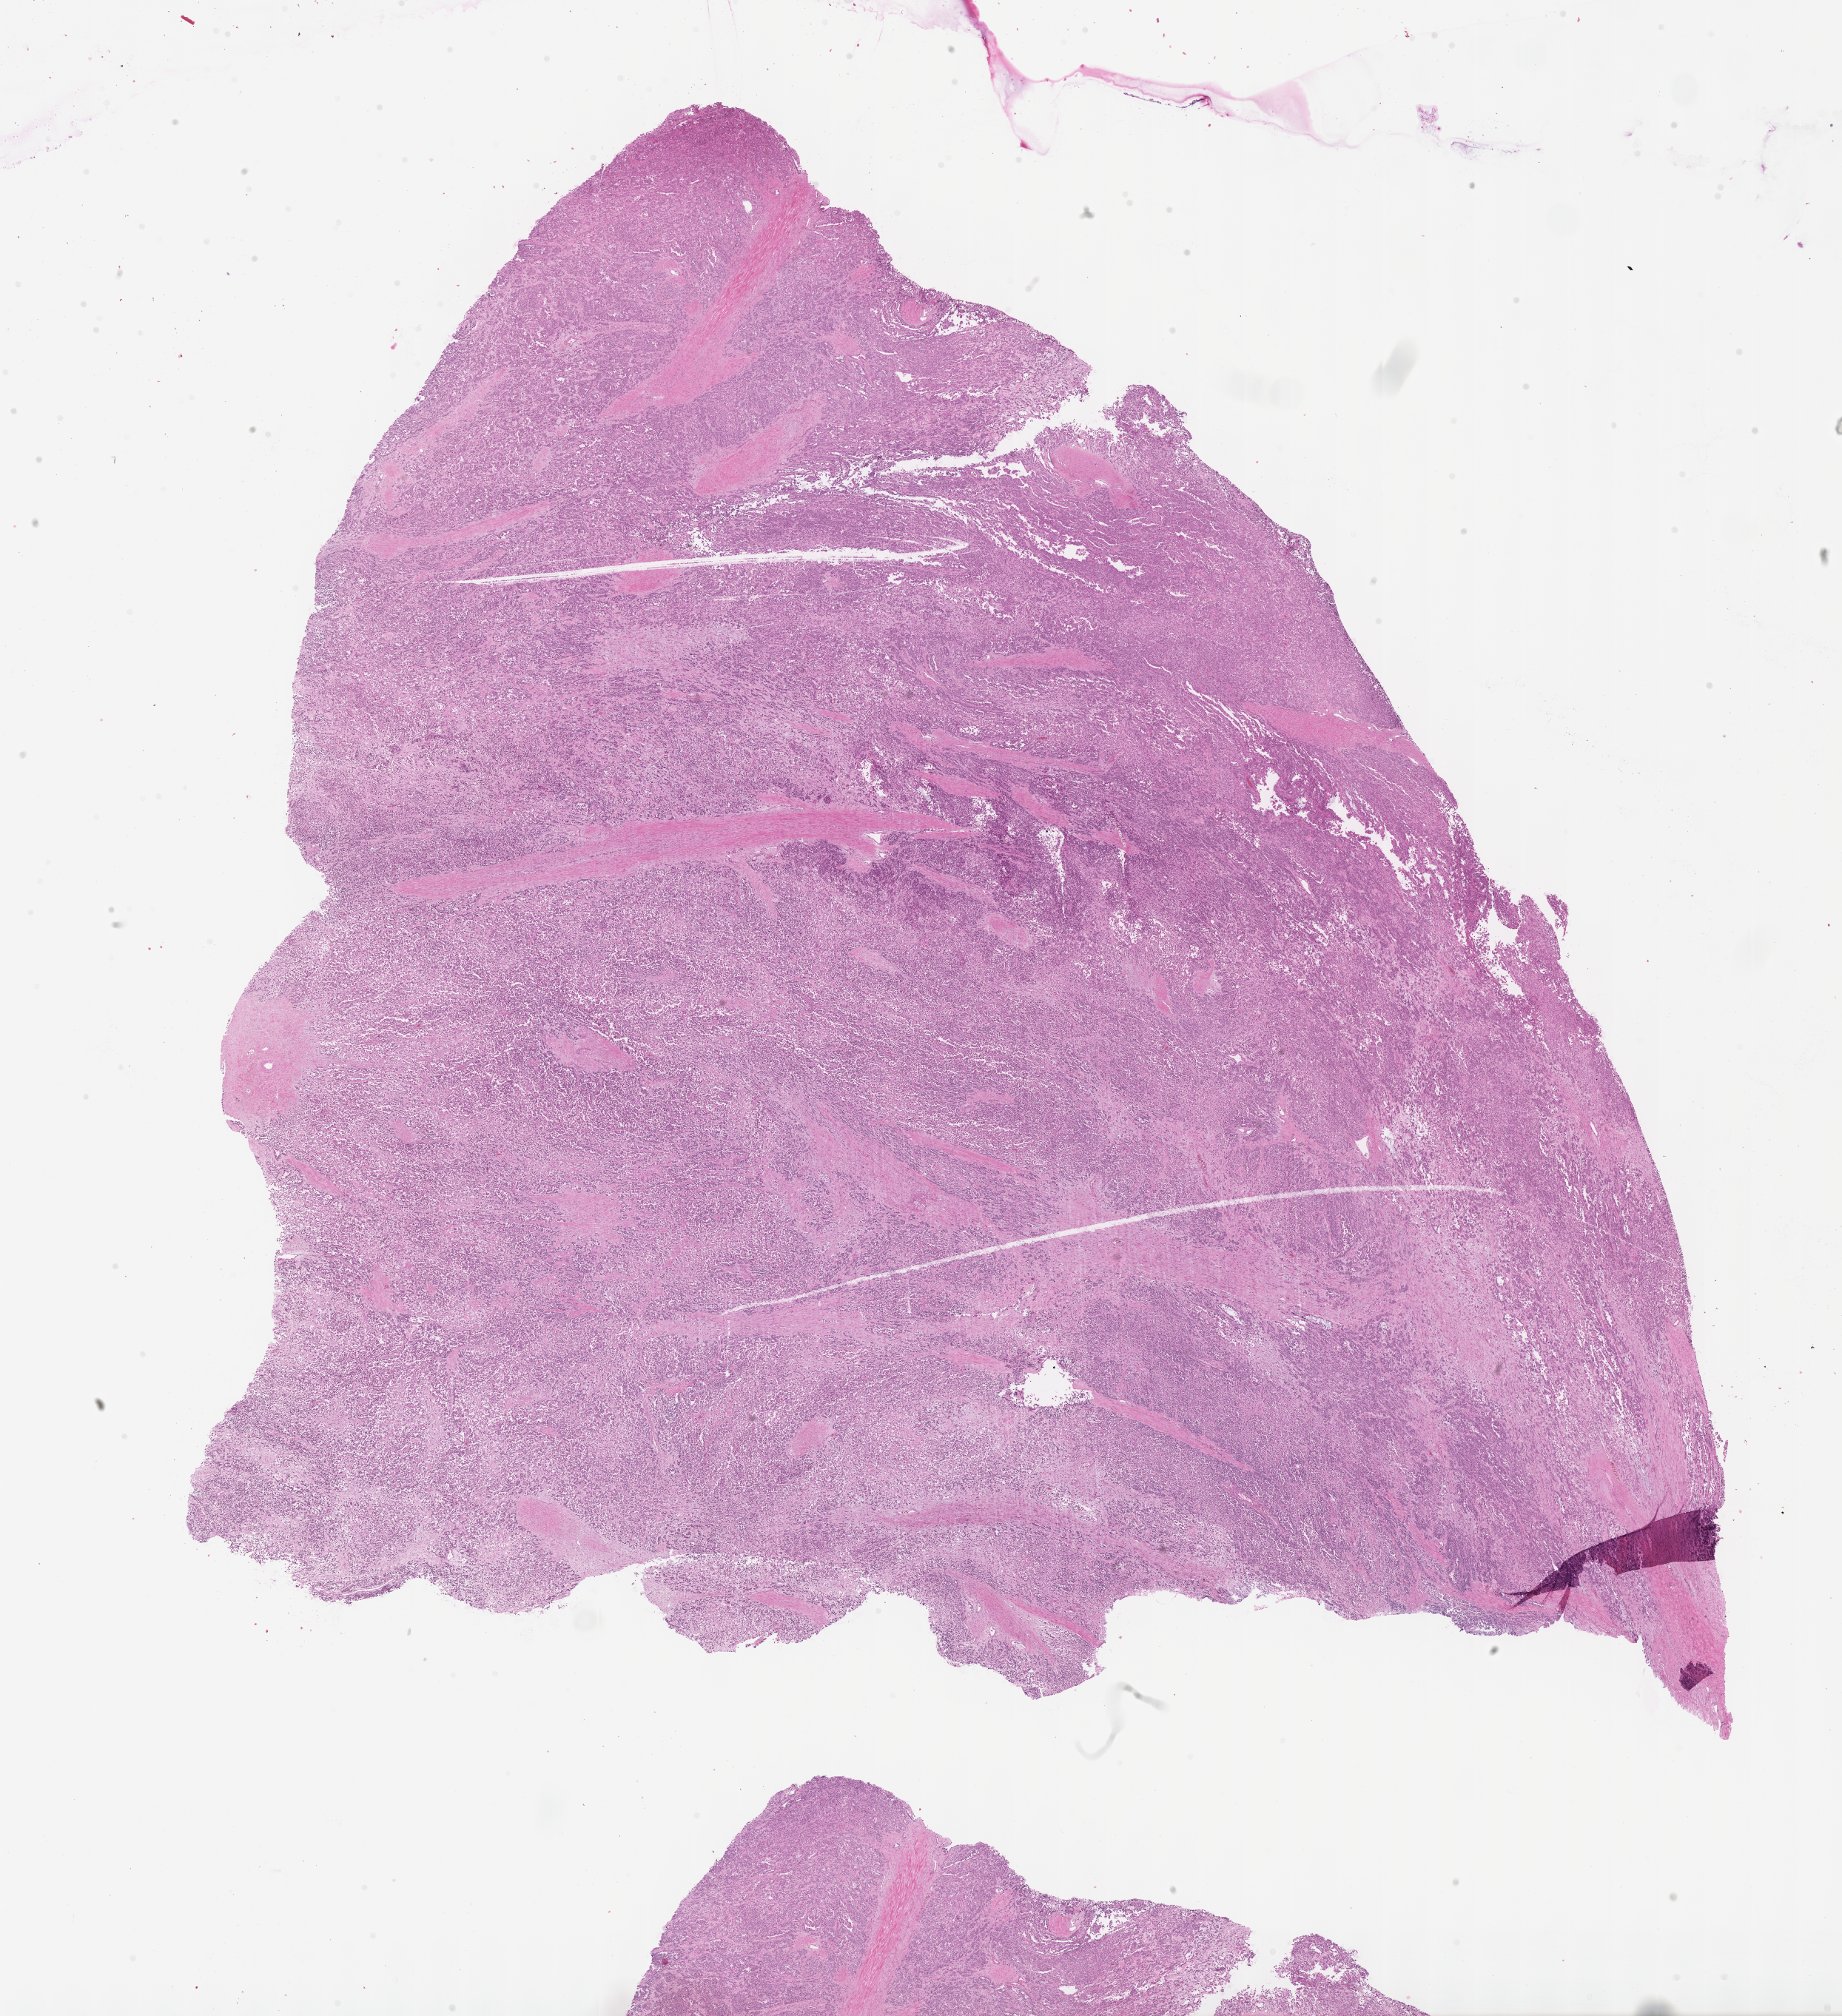
Hematoxylin and eosin (H&E) whole-slide image of tumor tissue, a low-resolution overview of the entire scanned area, about 20.1 x 22.0 mm. FFPE section. Site: vulva. Female patient, age at diagnosis 17.0 years.
Stage (as recorded): 1. Metastatic status at presentation (as recorded): non-metastatic. Diagnosis: rhabdomyosarcoma; histological classification: alveolar rhabdomyosarcoma.